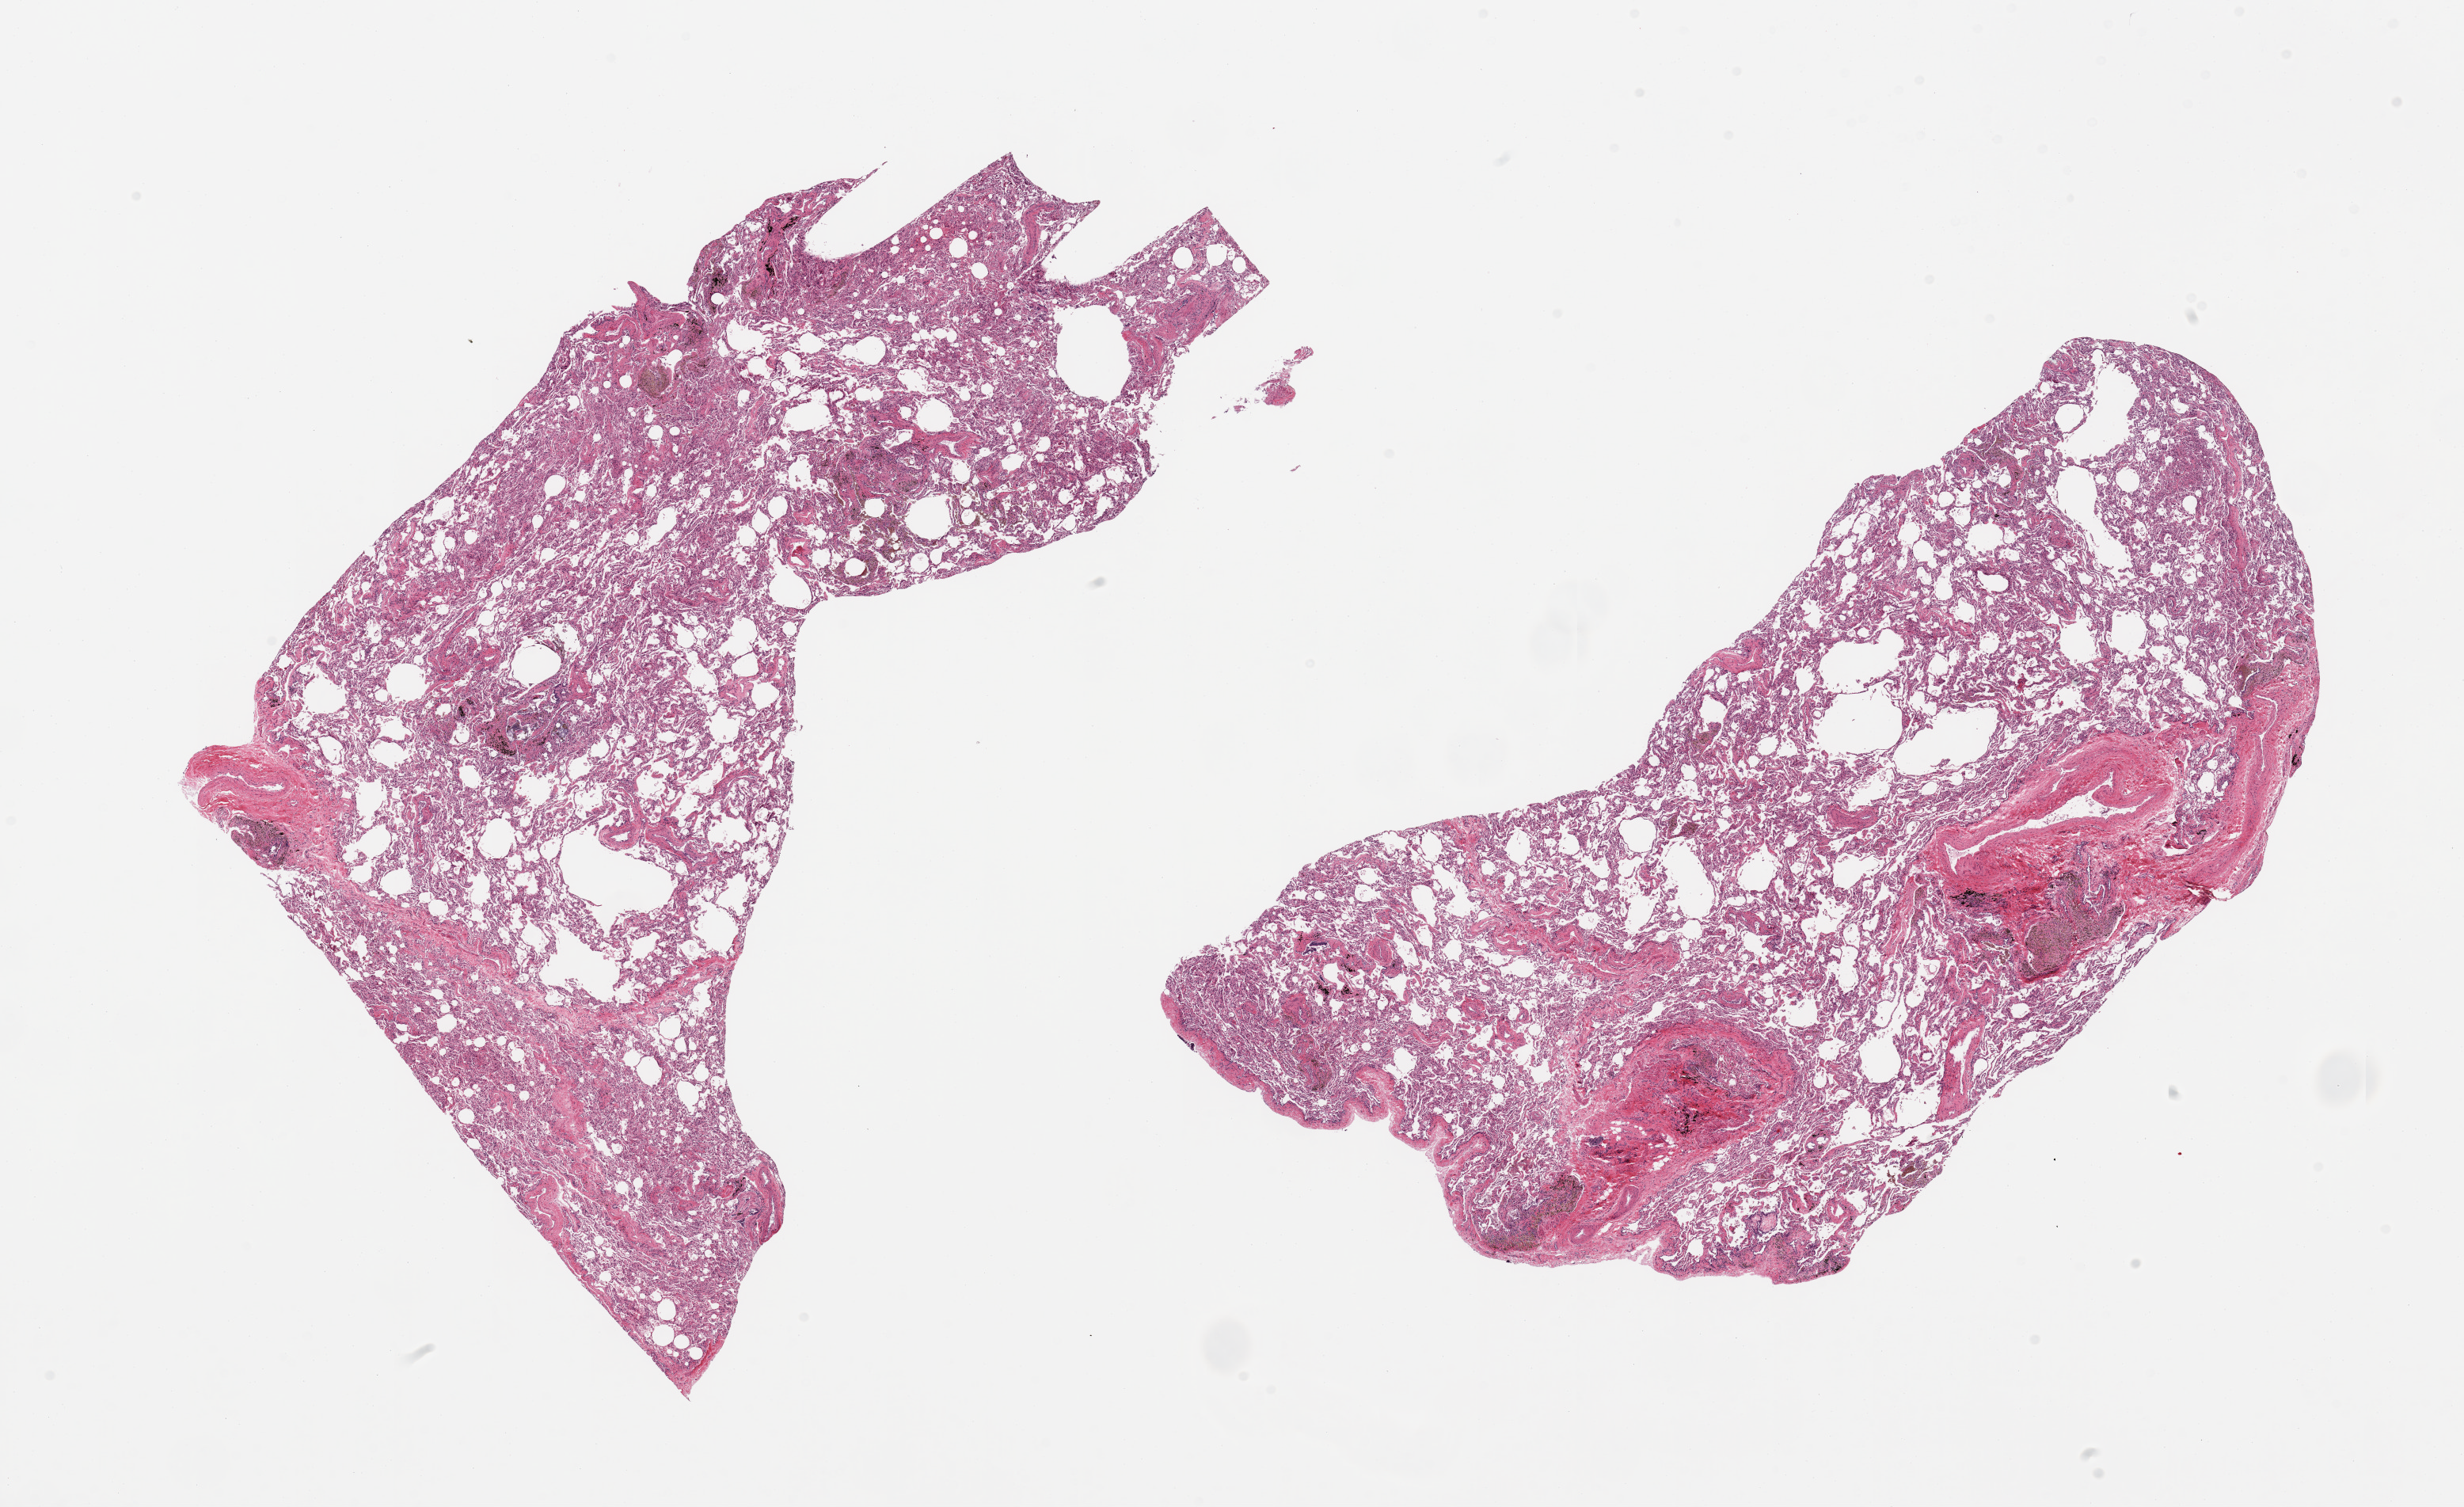
Digitized H&E-stained section, brightfield, low-resolution overview of the scanned area, about 24.6 x 15.0 mm (acquisition: 20x scan); PAXgene-fixed, paraffin-embedded tissue; sampled site (target tissue): lung; donor tissue sample. Male donor.
Review note (as recorded): 2 pieces; emphysema; moderate anthracotic pigment.